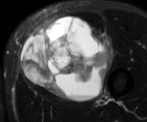
MRI of an extremity soft-tissue mass, one axial slice; position 30 of 52 along the scan axis; T2-weighted fat-saturated; MR volume resampled by the dataset authors to the PET/CT grid (not the native acquisition matrix); 3.27 mm slice thickness; 147 × 122 image matrix. Male patient. Case-level facts recorded for this patient, not image findings: histological type: pleiomorphic liposarcoma; grade: high; site of the primary tumour: left thigh.
Structures marked on this image (expert contour drawn on MRI and transferred to this co-registered scan by the dataset authors):
- gross tumour volume including surrounding oedema: bounding box <20,14,115,99> (left, top, right, bottom; pixels)
- gross tumour volume (mass): <21,16,111,100>